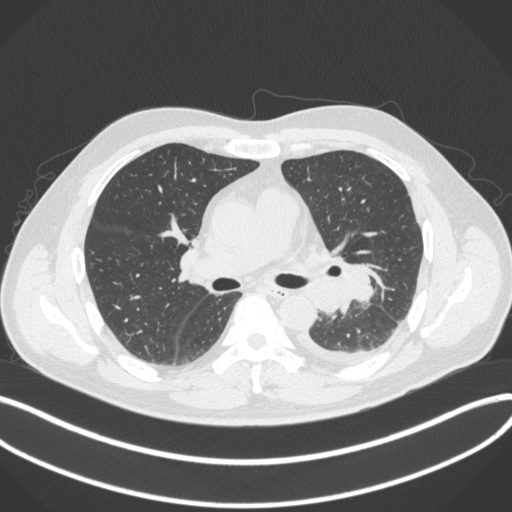
Chest CT, one axial slice; slice 213 of 350 in the series (ordered by position); 120 kVp; lung window (W 1500 / L -600 HU); 512 × 512 image matrix, field of view 400 × 400 mm. Male patient, age 58 years. Case-level facts recorded for this patient, not image findings: clinical TNM (as recorded): T3 N1 M1b; histopathological grade: G3.
Structures marked on this image (bounding box drawn by a radiologist):
- lung tumour (recorded histology: small cell carcinoma): bounding box [x1, y1, x2, y2] px = [348, 259, 383, 310]